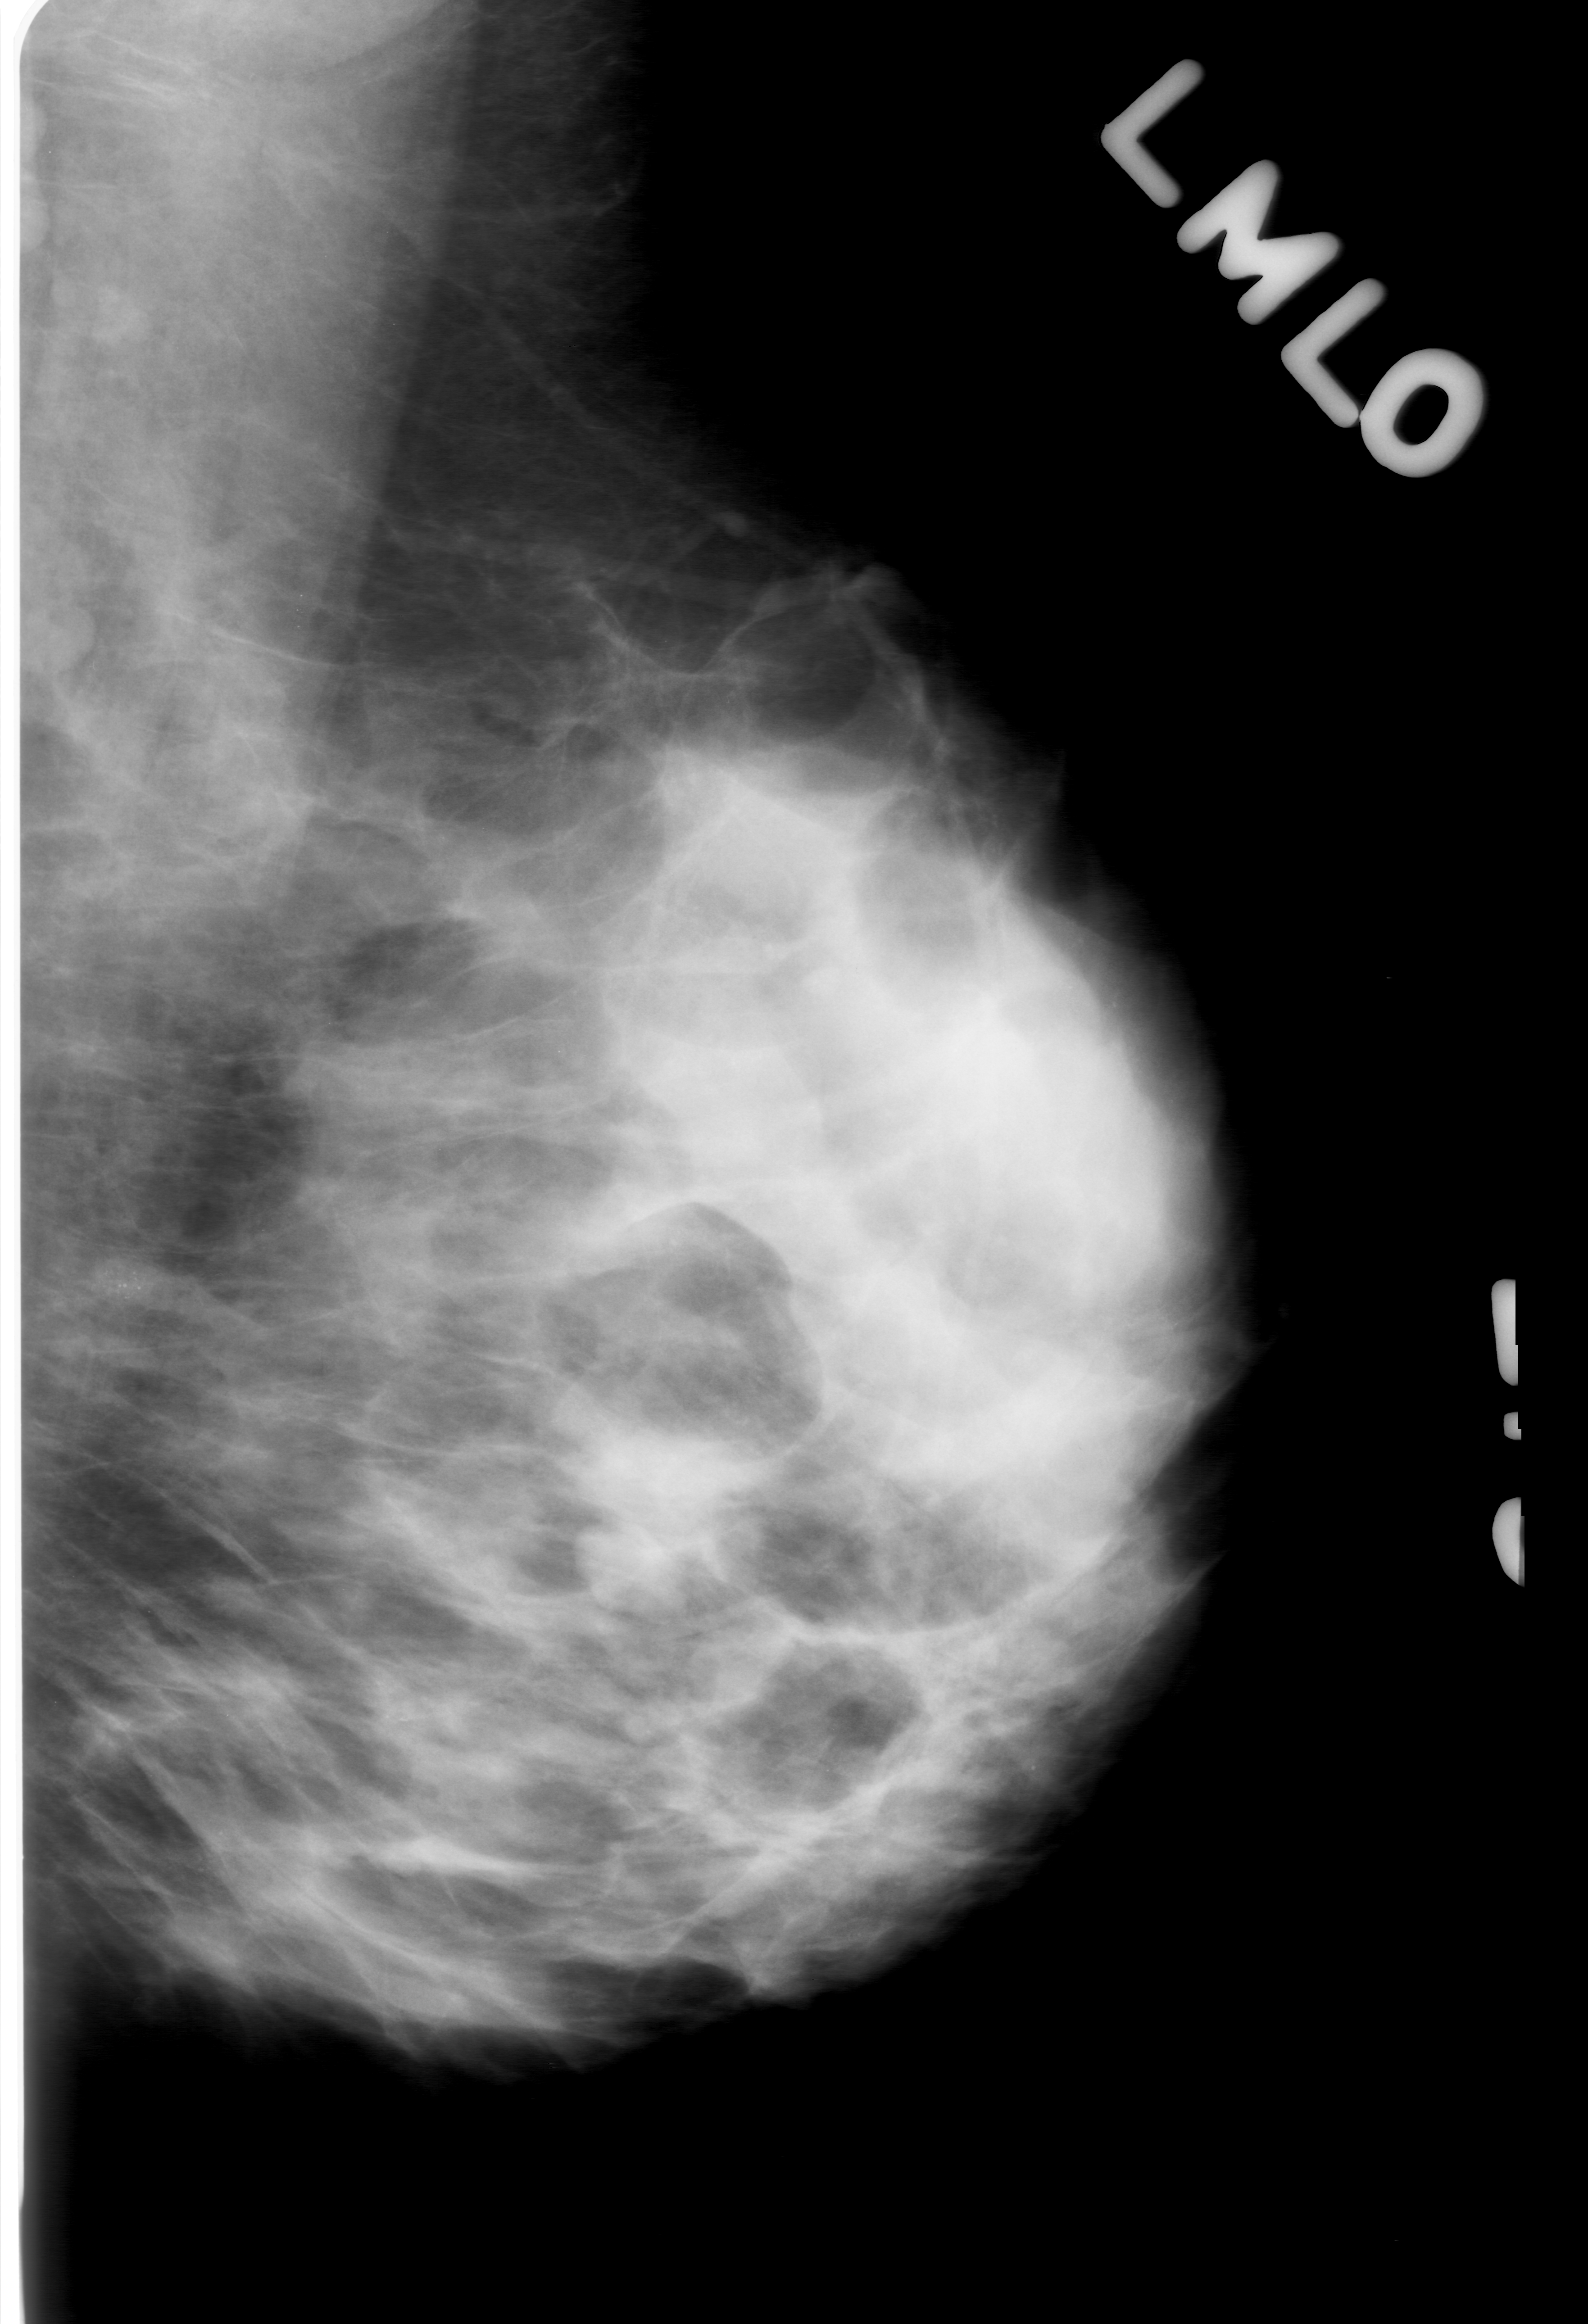
Scanned film-screen mammogram. Left breast. Mediolateral oblique (MLO) view. Breast composition: heterogeneously dense (BI-RADS density category 3 of 4). 1588 × 2324 image matrix.
Expert-marked regions of interest on this image (one box per marked abnormality):
- calcifications, morphology round and regular / pleomorphic, distribution clustered; BI-RADS assessment category 0 (incomplete: needs additional imaging); subtlety rating 3 on a 1 (subtle) to 5 (obvious) scale; pathology (as recorded): benign: bounding box (x1, y1, x2, y2) in pixels: (80, 1195, 250, 1363)